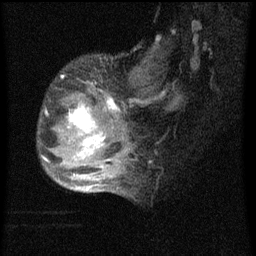
Breast MRI (dynamic contrast-enhanced), one sagittal slice; slice 21 of 60 in the series (ordered by position); dynamic contrast-enhanced series, image 2 of 4 at this slice position (ordered by acquisition); 1.5 T; TE 4.2 ms, TR 8 ms; 2 mm slice thickness; 256 × 256 image matrix. Female patient, age 50 years.
Annotated regions visible in this slice (semi-automatic segmentation, software-assisted and operator-edited):
- analysis volume of interest (the breast-tissue region the enhancement analysis was run in; not a lesion): bounding box <40,68,124,177> (left, top, right, bottom; pixels)
- tumour enhancement mask (voxels above the 70 % enhancement threshold inside the analysis volume of interest): <67,98,121,177>